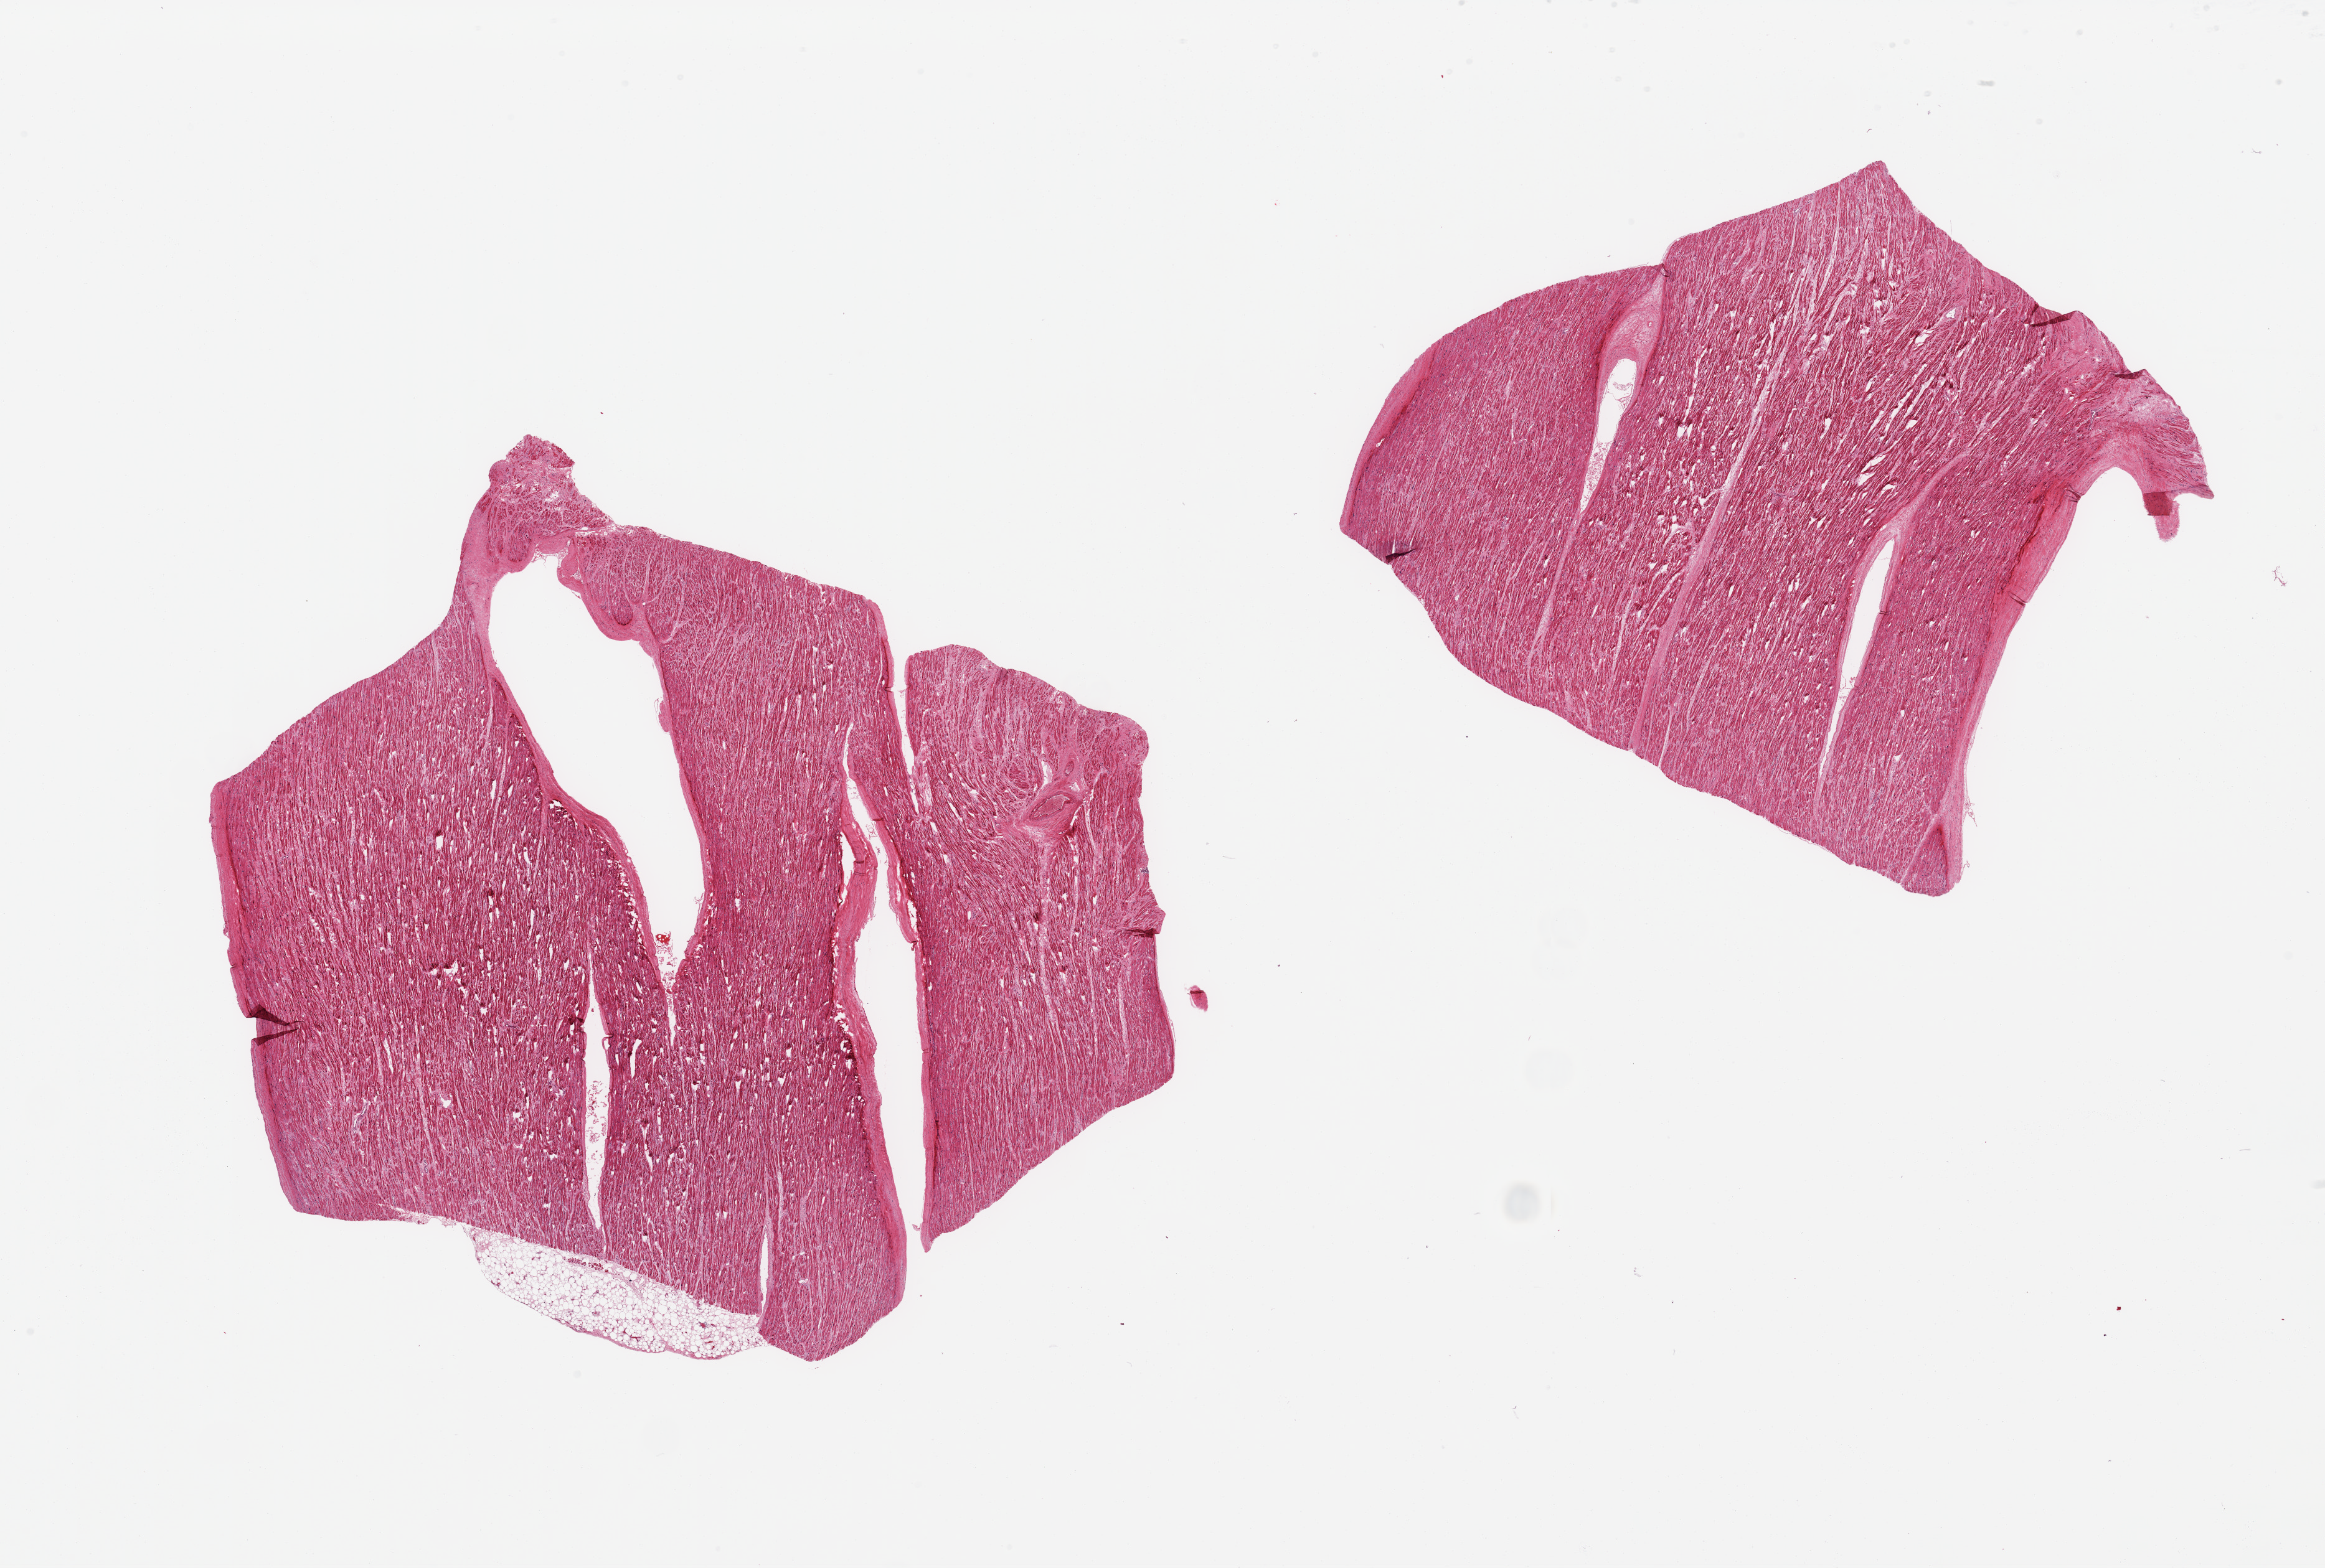
Whole-slide image, haematoxylin and eosin stain — shown as a low-resolution overview of the whole scanned area (about 29.5 x 19.9 mm, from a 20x scan); PAXgene-fixed paraffin-embedded (PFPE) section; sampled site (target tissue): auricular appendage; tissue donor sample. Donor: male.
- reviewer comment on this tissue sample: 2 pieces; trace of external fat